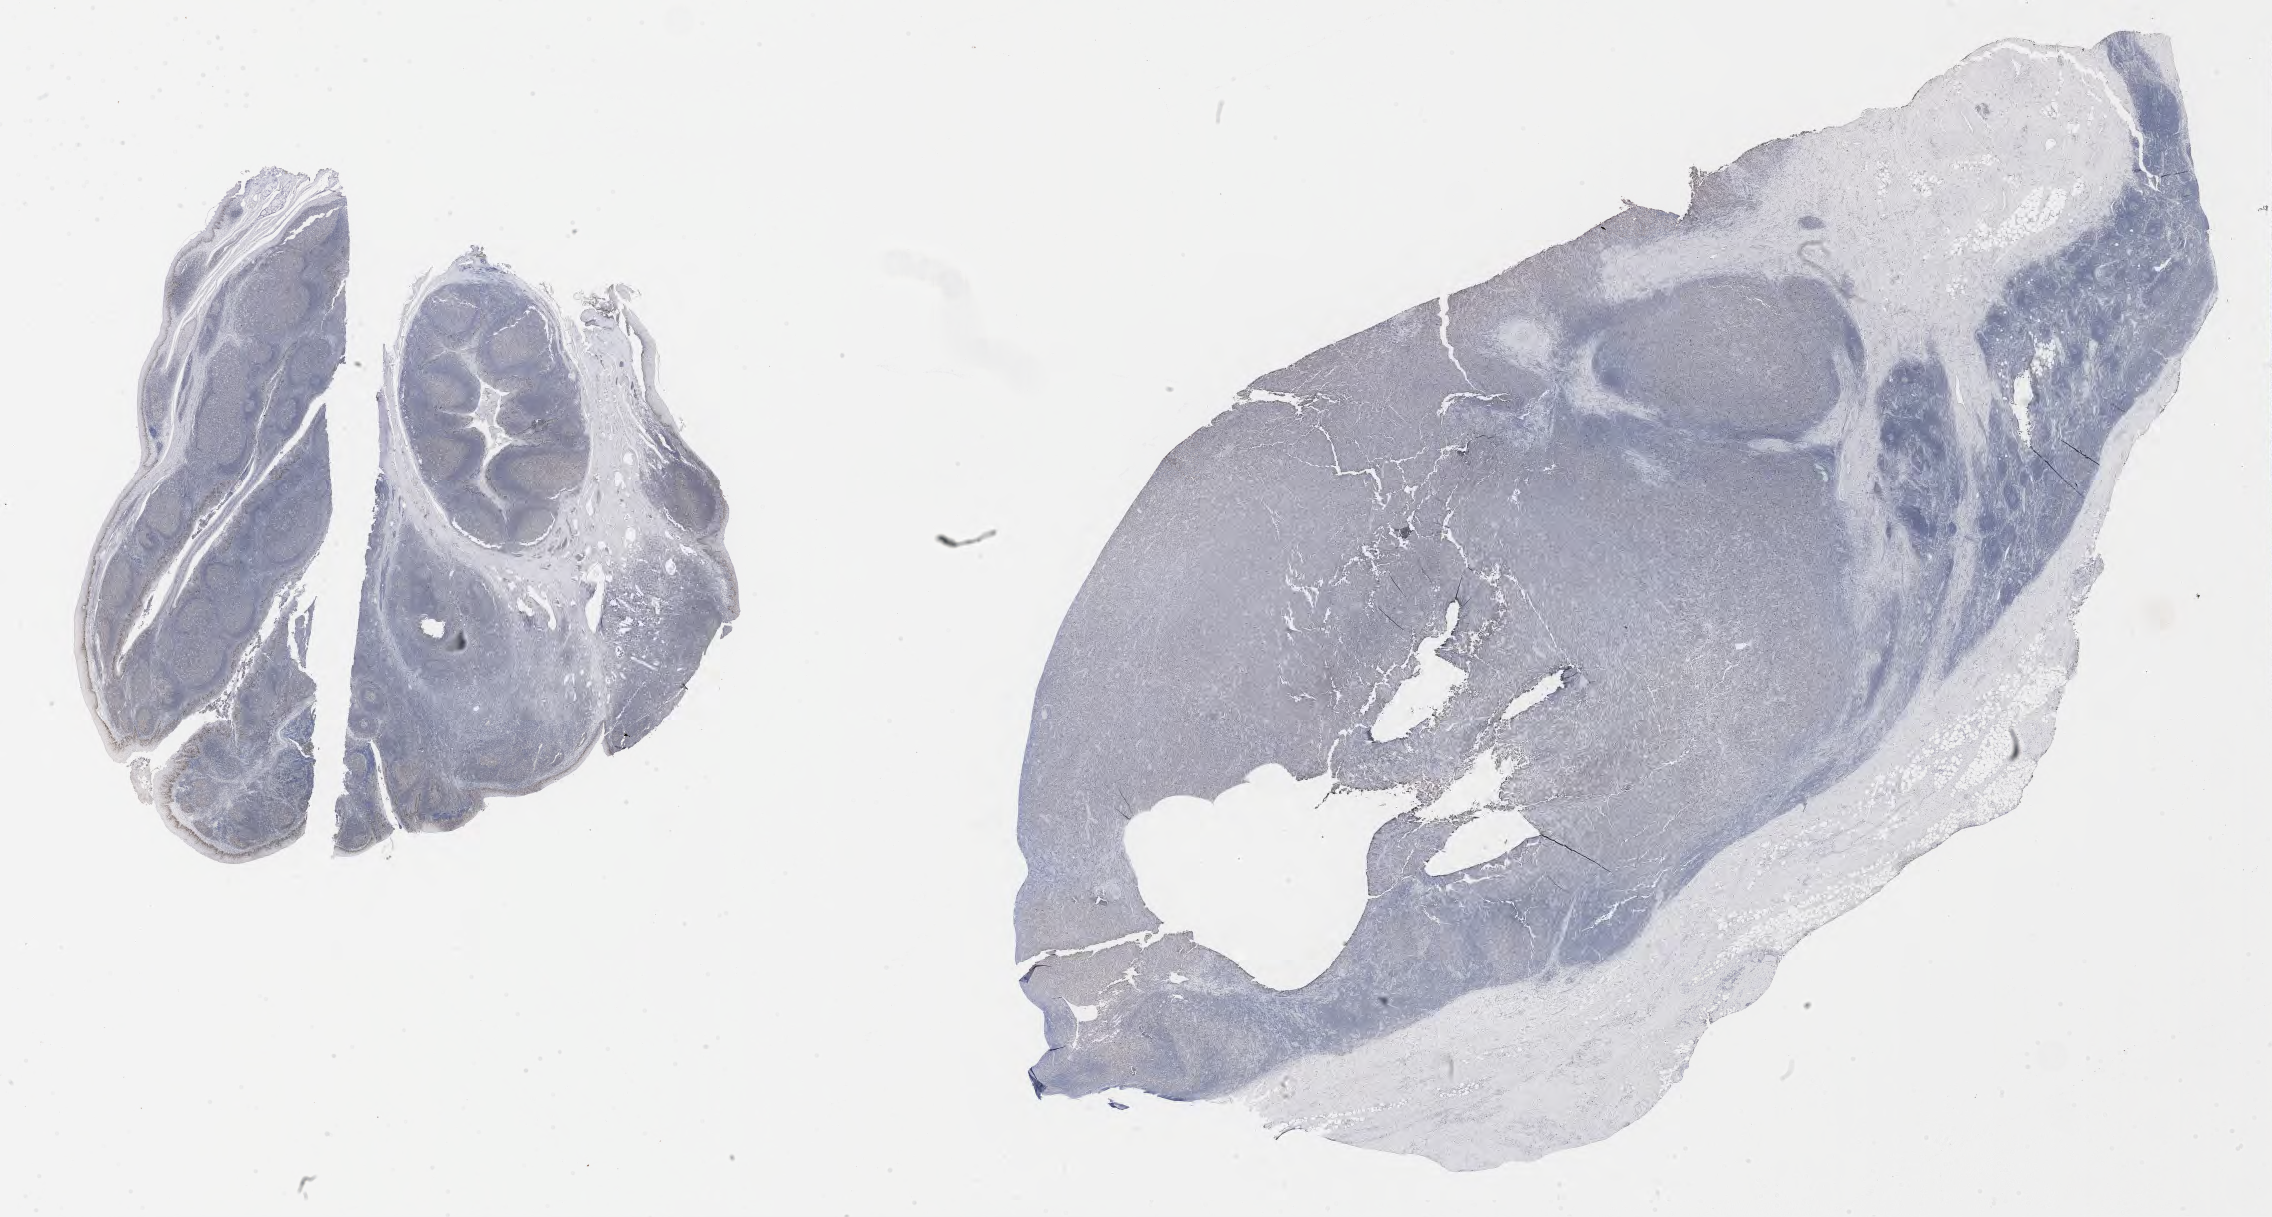
IHC for p53, whole-slide image, low-resolution overview of the scanned area, about 36.7 x 19.7 mm; specimen: tumor tissue; anatomic site: lymph node. Male patient, aged 60.
Diagnosis: Diffuse large B-cell lymphoma, NOS.